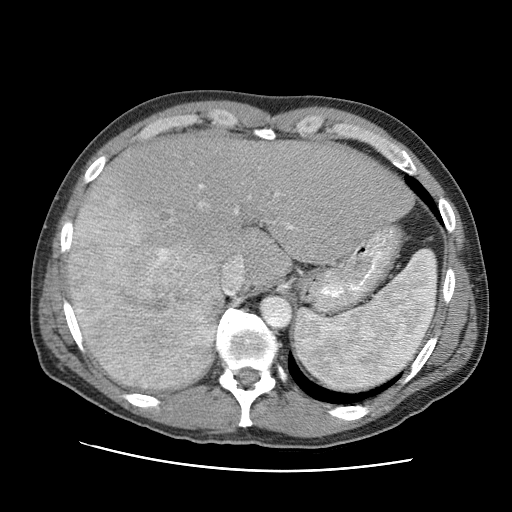
Contrast-enhanced abdominal CT (liver protocol), one axial slice; slice 69 of 95 in the series (ordered by position); 120 kVp; one of 2 acquisitions stored at this slice position; soft-tissue window (W 400 / L 40 HU); 512 × 512 image matrix. Case-level facts recorded for this patient, not image findings: diagnosis: hepatocellular carcinoma (patient treated with transarterial chemoembolisation; whether this scan precedes or follows treatment is not stated here); TNM stage (as recorded): Stage-IVA; Child-Pugh class: A; tumour nodularity: multinodular.
Annotated regions visible in this slice (semi-automatic segmentation, software-assisted and operator-edited):
- liver parenchyma outside the tumour (the mass and vessels are separate outlines, so this box may not span the whole liver): bounding box [x1, y1, x2, y2] px = [68, 134, 414, 343]
- mass: [68, 188, 223, 392]
- liver vessels: [74, 184, 294, 335]